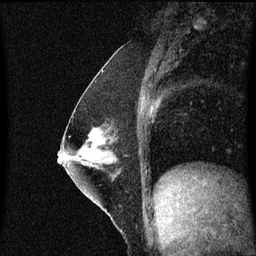
Breast MRI (dynamic contrast-enhanced), one sagittal slice. Position 27 of 60 along the scan axis. Dynamic contrast-enhanced series, image 2 of 3 at this slice position (ordered by acquisition). 1.5 T. TE 4.2 ms, TR 8.4 ms. 2 mm slice thickness. 256 × 256 image matrix, field of view 200 × 200 mm. Patient: female, 52 years. From the clinical record (not read from this slice): setting: breast cancer imaged before/during neoadjuvant chemotherapy; receptor status: HER2-positive.
Annotated regions visible in this slice (semi-automatic segmentation, software-assisted and operator-edited):
- analysis volume of interest (the breast-tissue region the enhancement analysis was run in; not a lesion): box from (x=71, y=118) to (x=123, y=187) px
- tumour enhancement mask (voxels above the 70 % enhancement threshold inside the analysis volume of interest): (x=88, y=130)–(x=99, y=141)